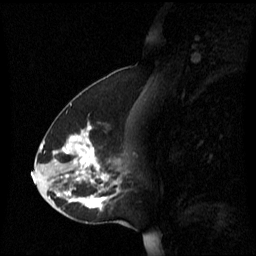
Breast MRI (dynamic contrast-enhanced), one sagittal slice. Slice 27 of 60 in the series (ordered by position). Dynamic contrast-enhanced series, image 2 of 3 at this slice position (ordered by acquisition). 1.5 T. TE 4.2 ms, TR 8.4 ms. 2.2 mm slice thickness. 256 × 256 image matrix, field of view 240 × 240 mm. Female patient, age 45 years. Case-level facts recorded for this patient, not image findings: setting: breast cancer imaged before/during neoadjuvant chemotherapy; receptor status: HR-positive, HER2-negative.
Annotated regions visible in this slice (semi-automatic segmentation, software-assisted and operator-edited):
- analysis volume of interest (the breast-tissue region the enhancement analysis was run in; not a lesion): bounding box [x1, y1, x2, y2] px = [38, 122, 129, 221]
- tumour enhancement mask (voxels above the 70 % enhancement threshold inside the analysis volume of interest): [56, 124, 119, 211]